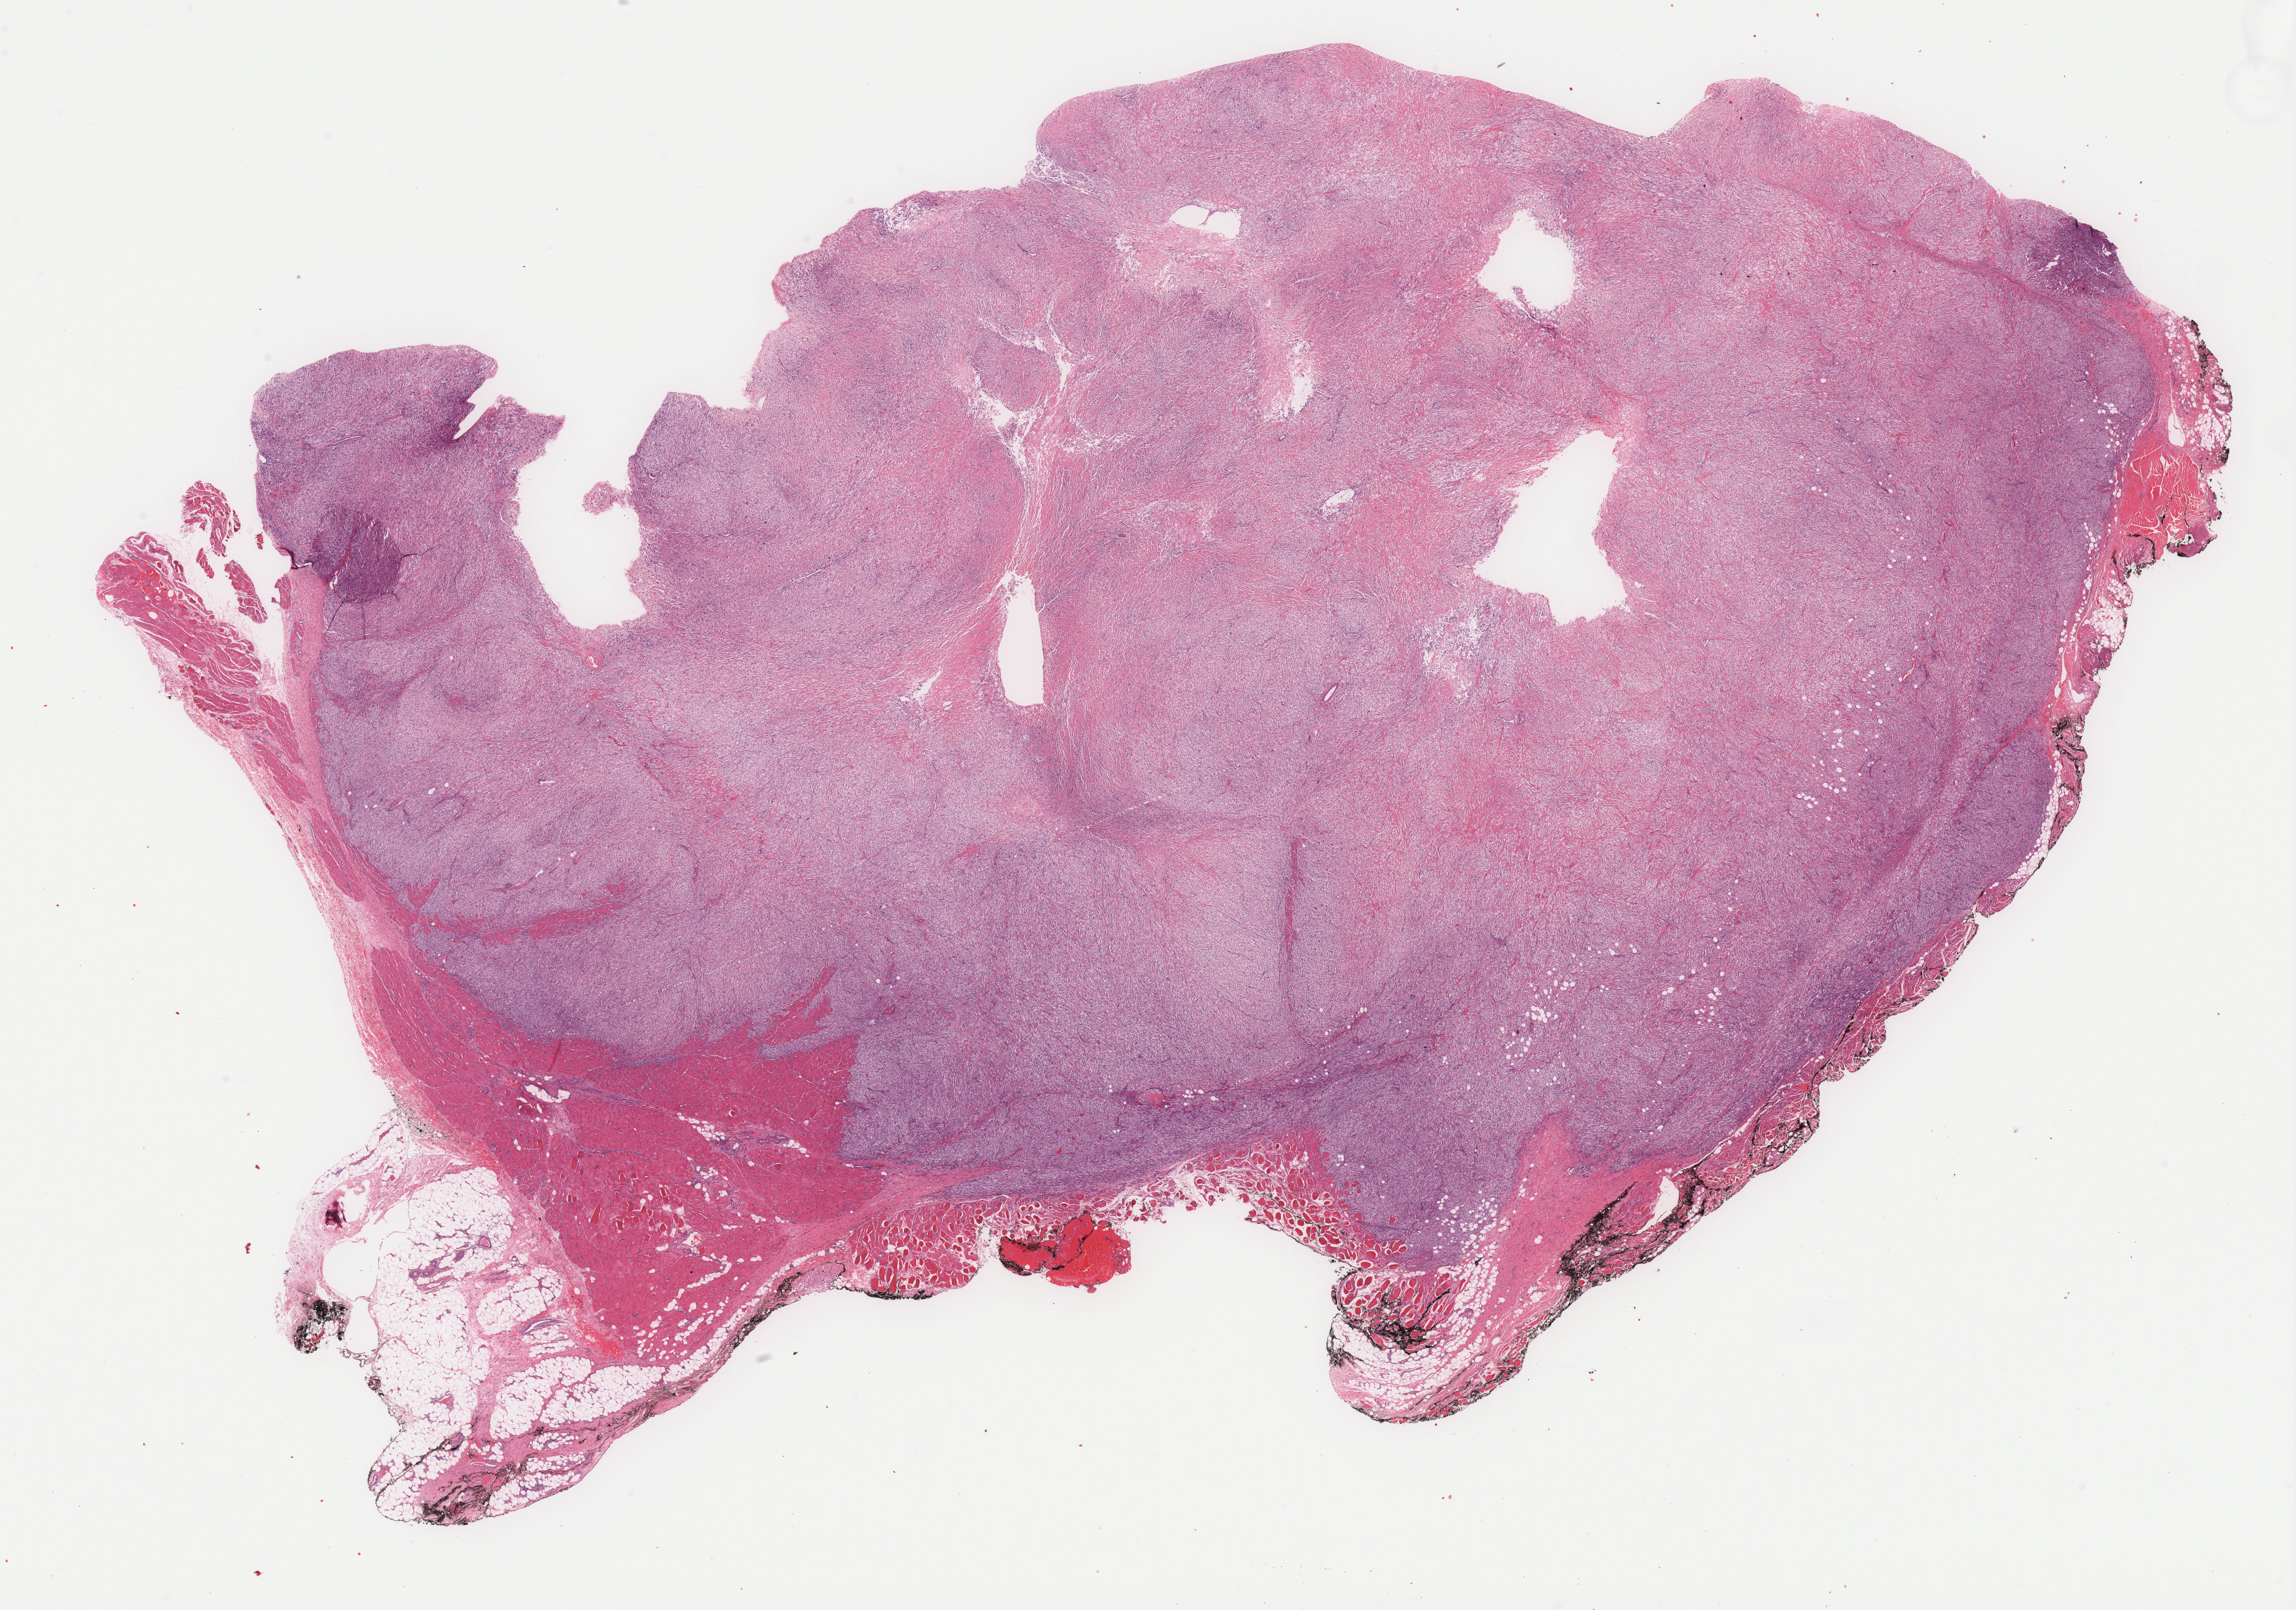
Whole-slide histology image, Hematoxylin and eosin (H&E) stained — low-resolution overview of the scanned area, about 26.2 x 18.3 mm, formalin-fixed paraffin-embedded (FFPE) diagnostic section, connective, subcutaneous and other soft tissues, primary tumour sample. Patient: male, age at initial diagnosis 80 years.
Histologic diagnosis: Liposarcoma, NOS (connective, subcutaneous and other soft tissues, NOS).